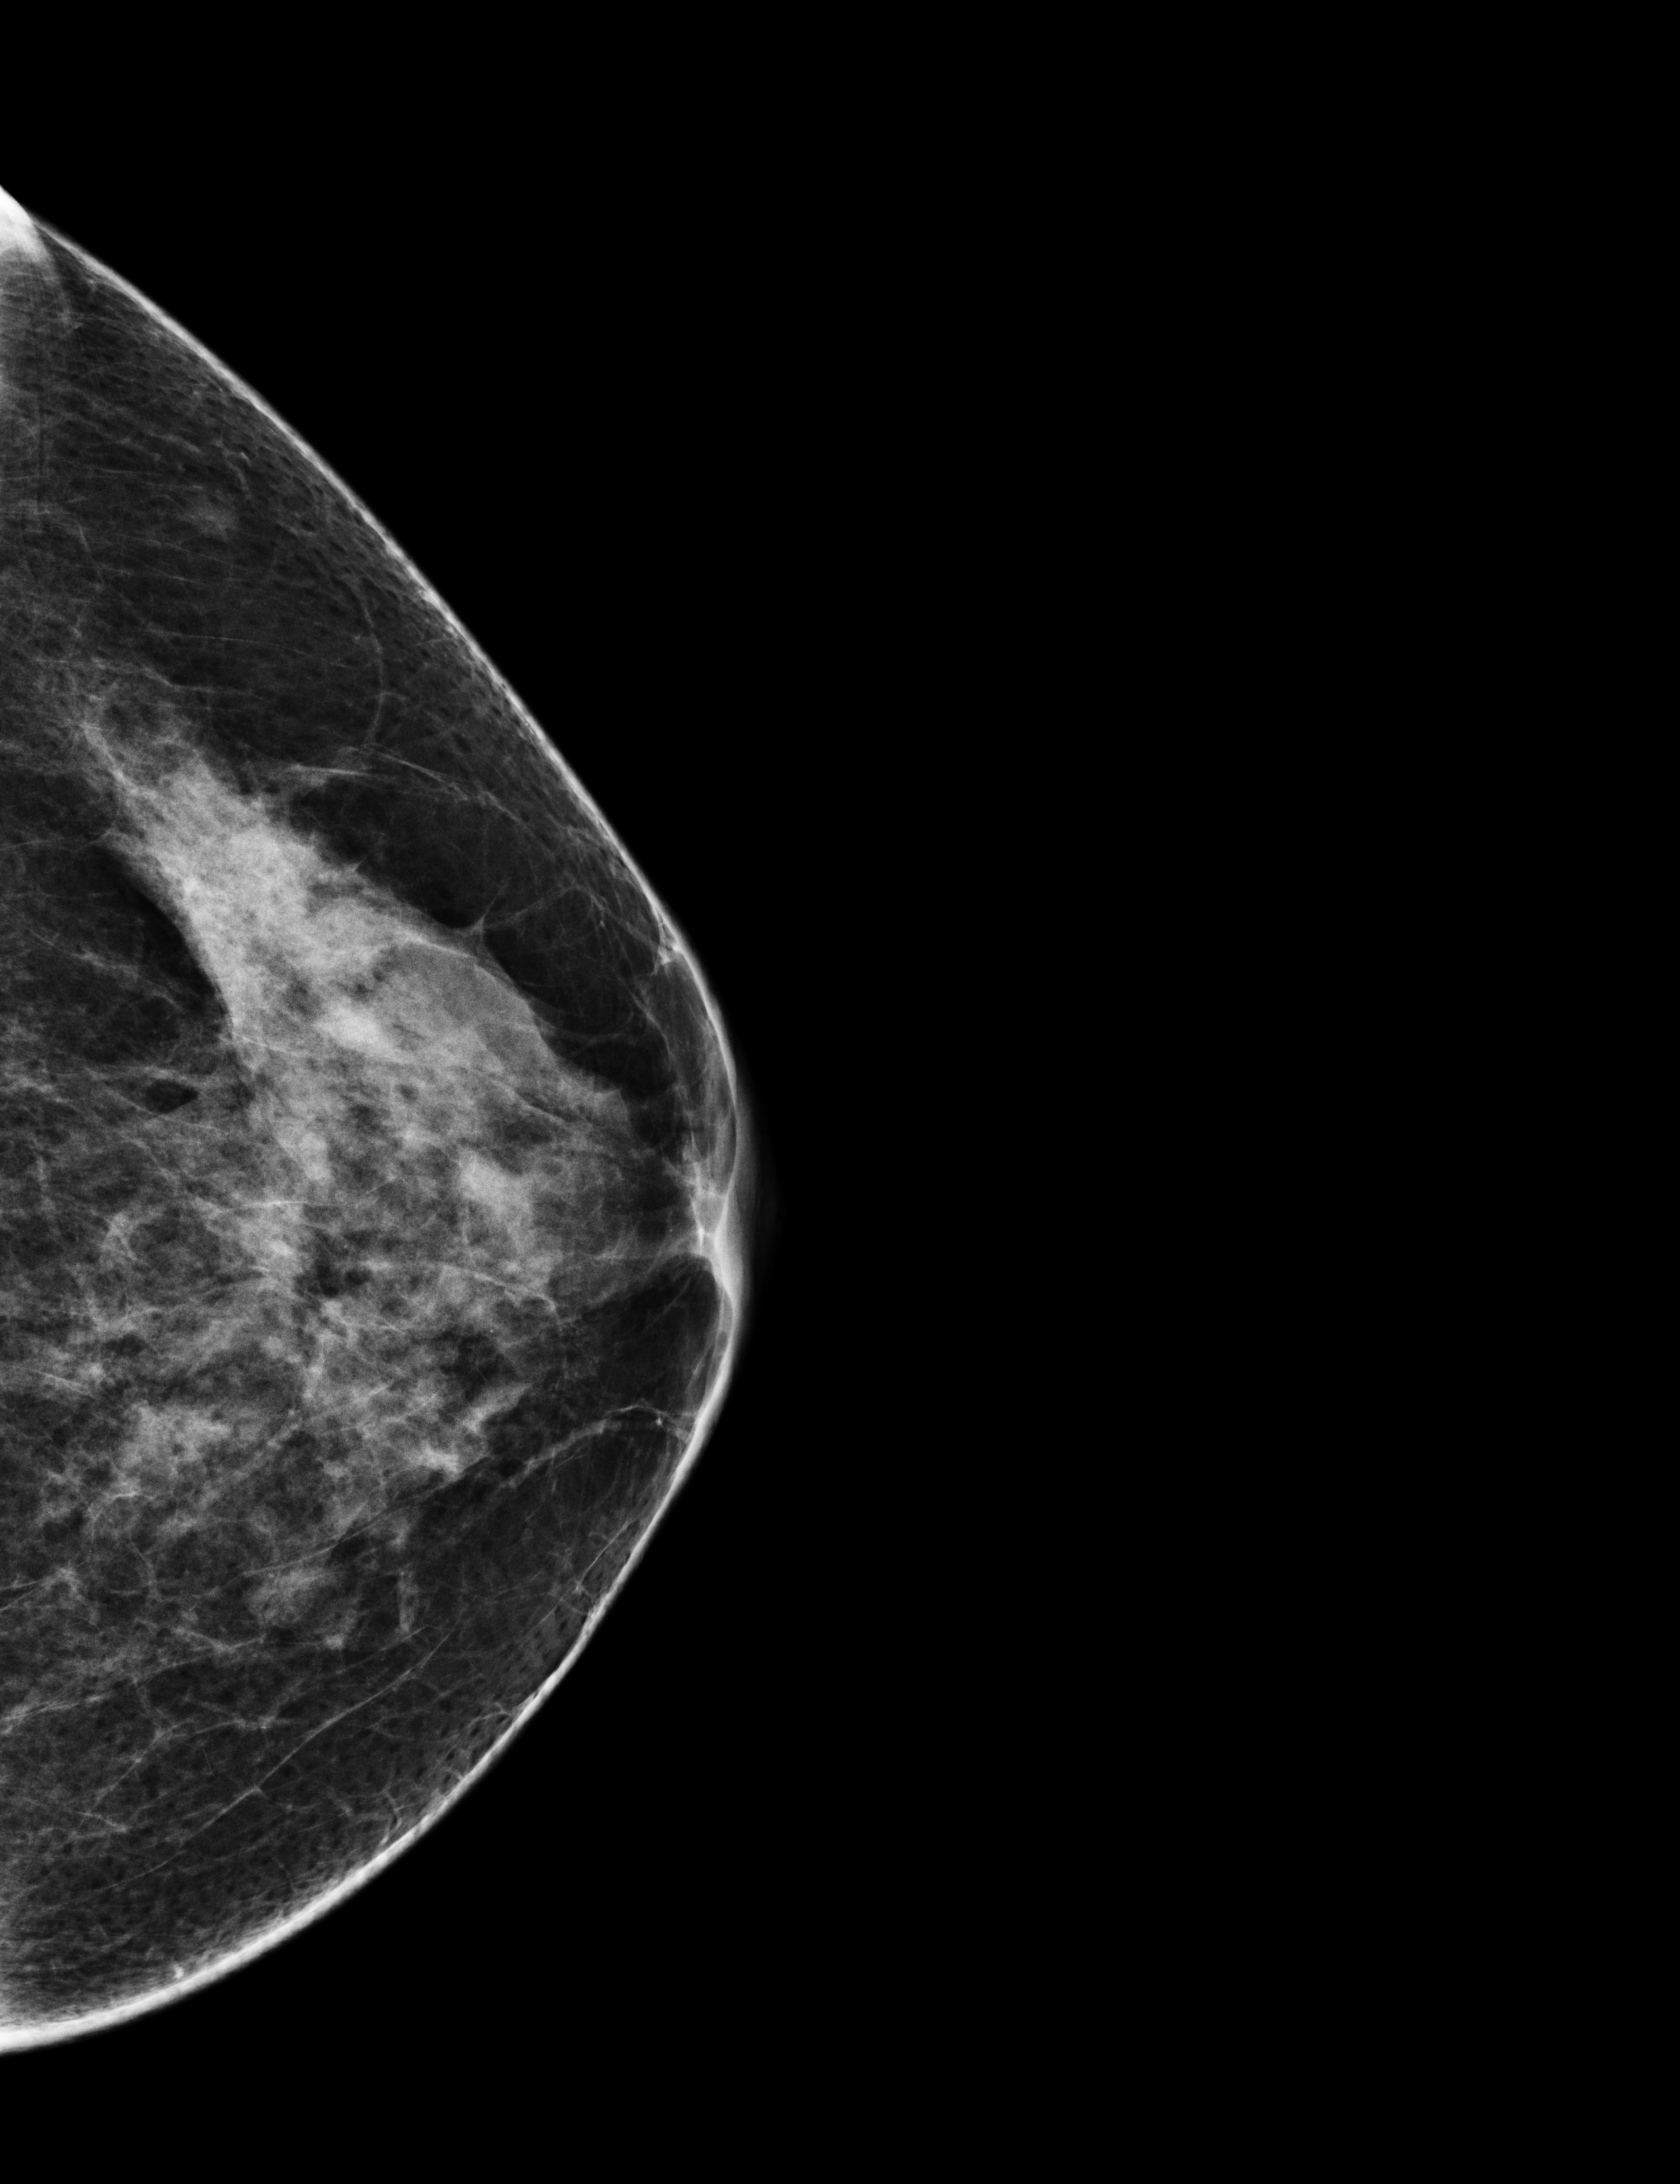
Full-field digital mammogram (FFDM), left breast, CC view, screening examination, system: Selenia Dimensions. Patient: female, 58 years.
Breast density at the screening exam (both breasts): heterogeneously dense (BI-RADS density category c). Final BI-RADS assessment for this screening round (tomosynthesis exam, both breasts): category 4. Recall: recalled for additional imaging after this screen.